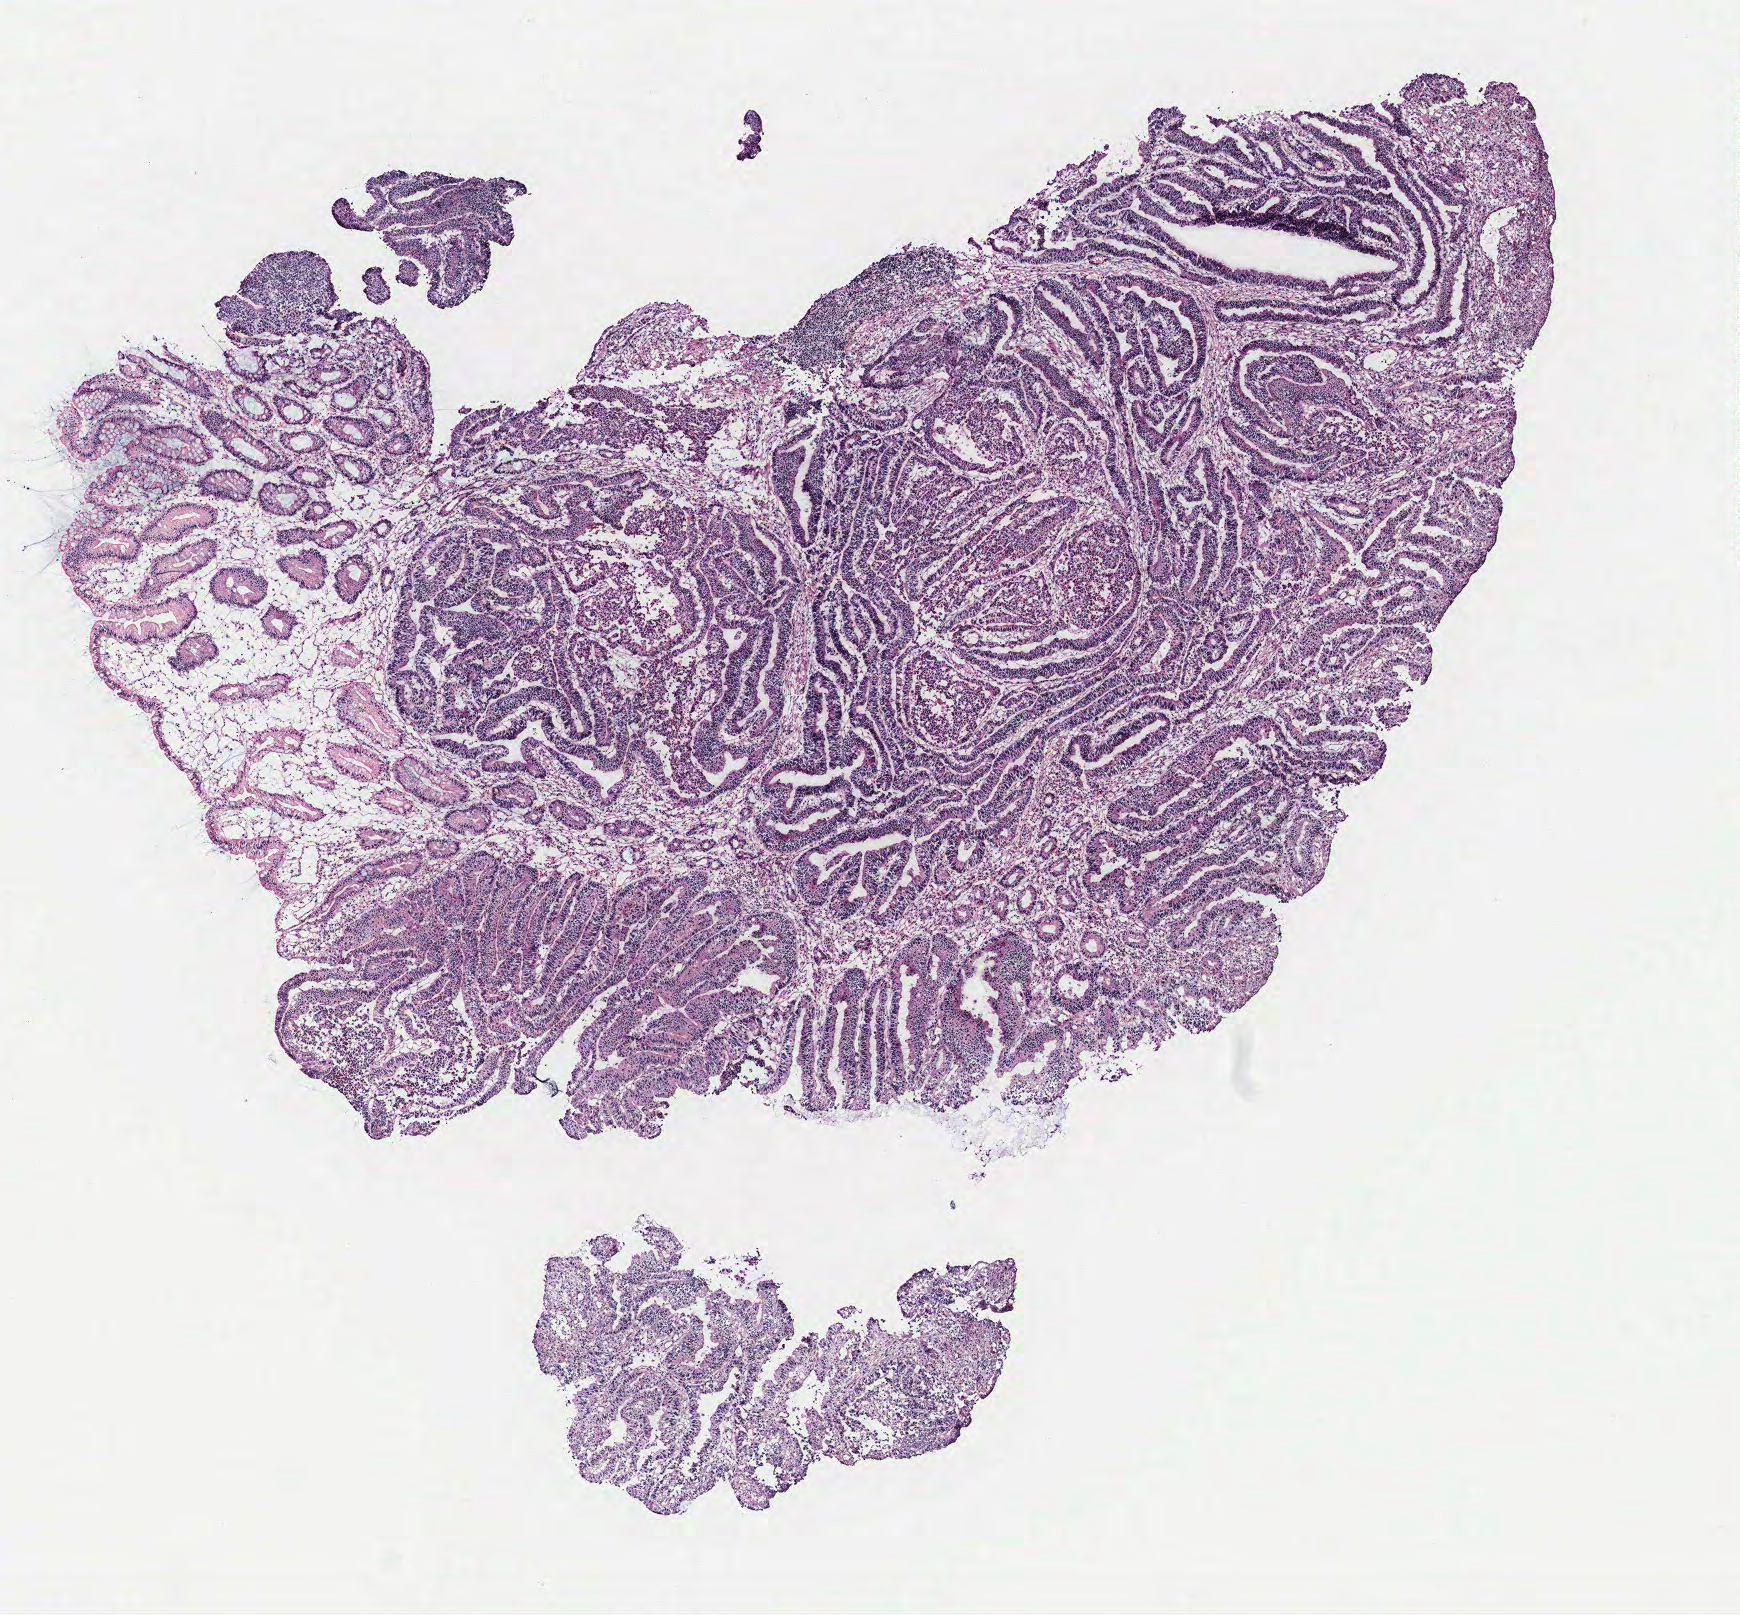
Whole-slide histology image, H&E, whole scanned area (about 7.0 x 6.5 mm) shown as a low-resolution overview, colon, tissue type not recorded.
• patient diagnosis (cohort enrolment): colon cancer (colon)